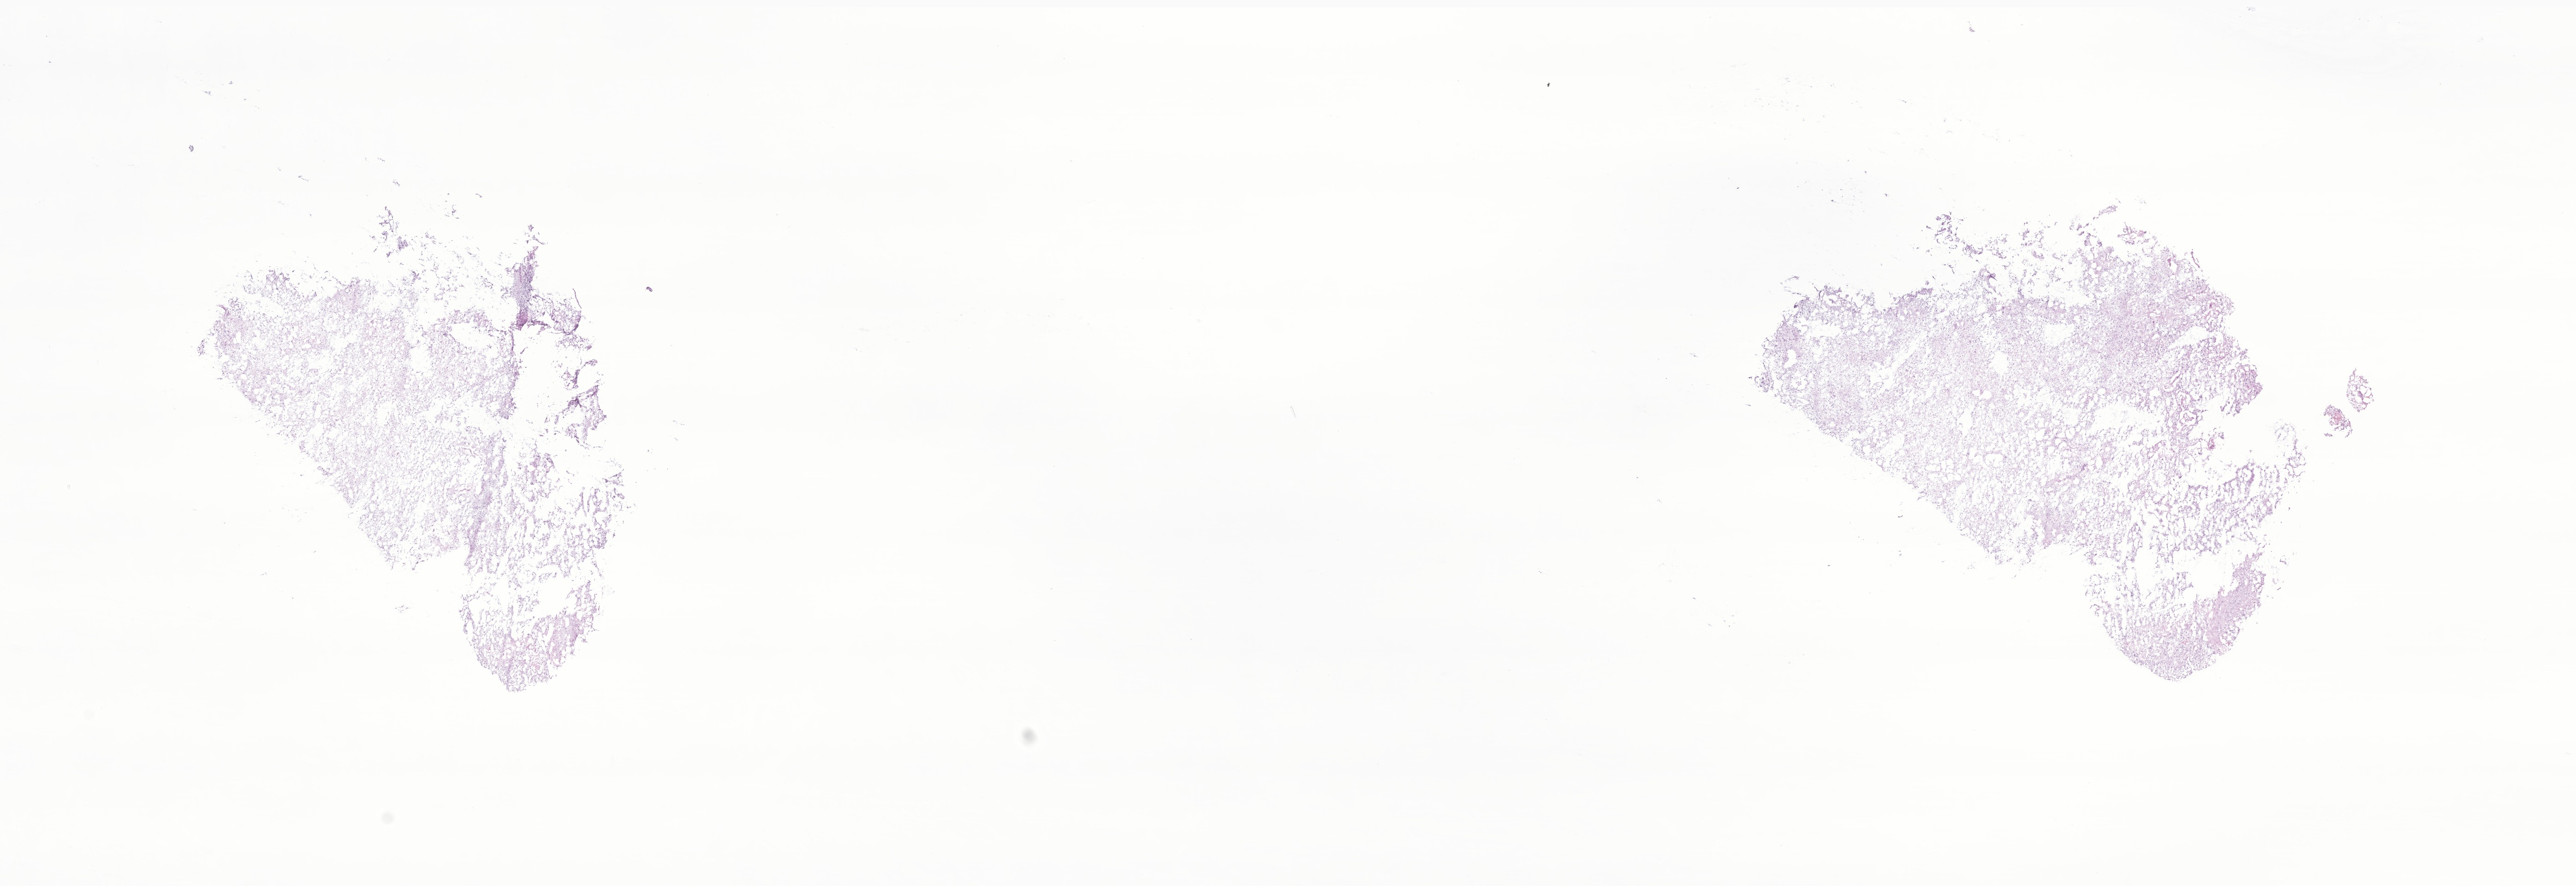
Whole-slide image, H&E stain of tumor tissue from the brain — shown as a low-resolution overview of the whole scanned area (about 23.5 x 8.1 mm), frozen section. Male patient, age 218 months (18 years 2 months).
Diagnosis (ICD-O-3 morphology term): Pilocytic astrocytoma.